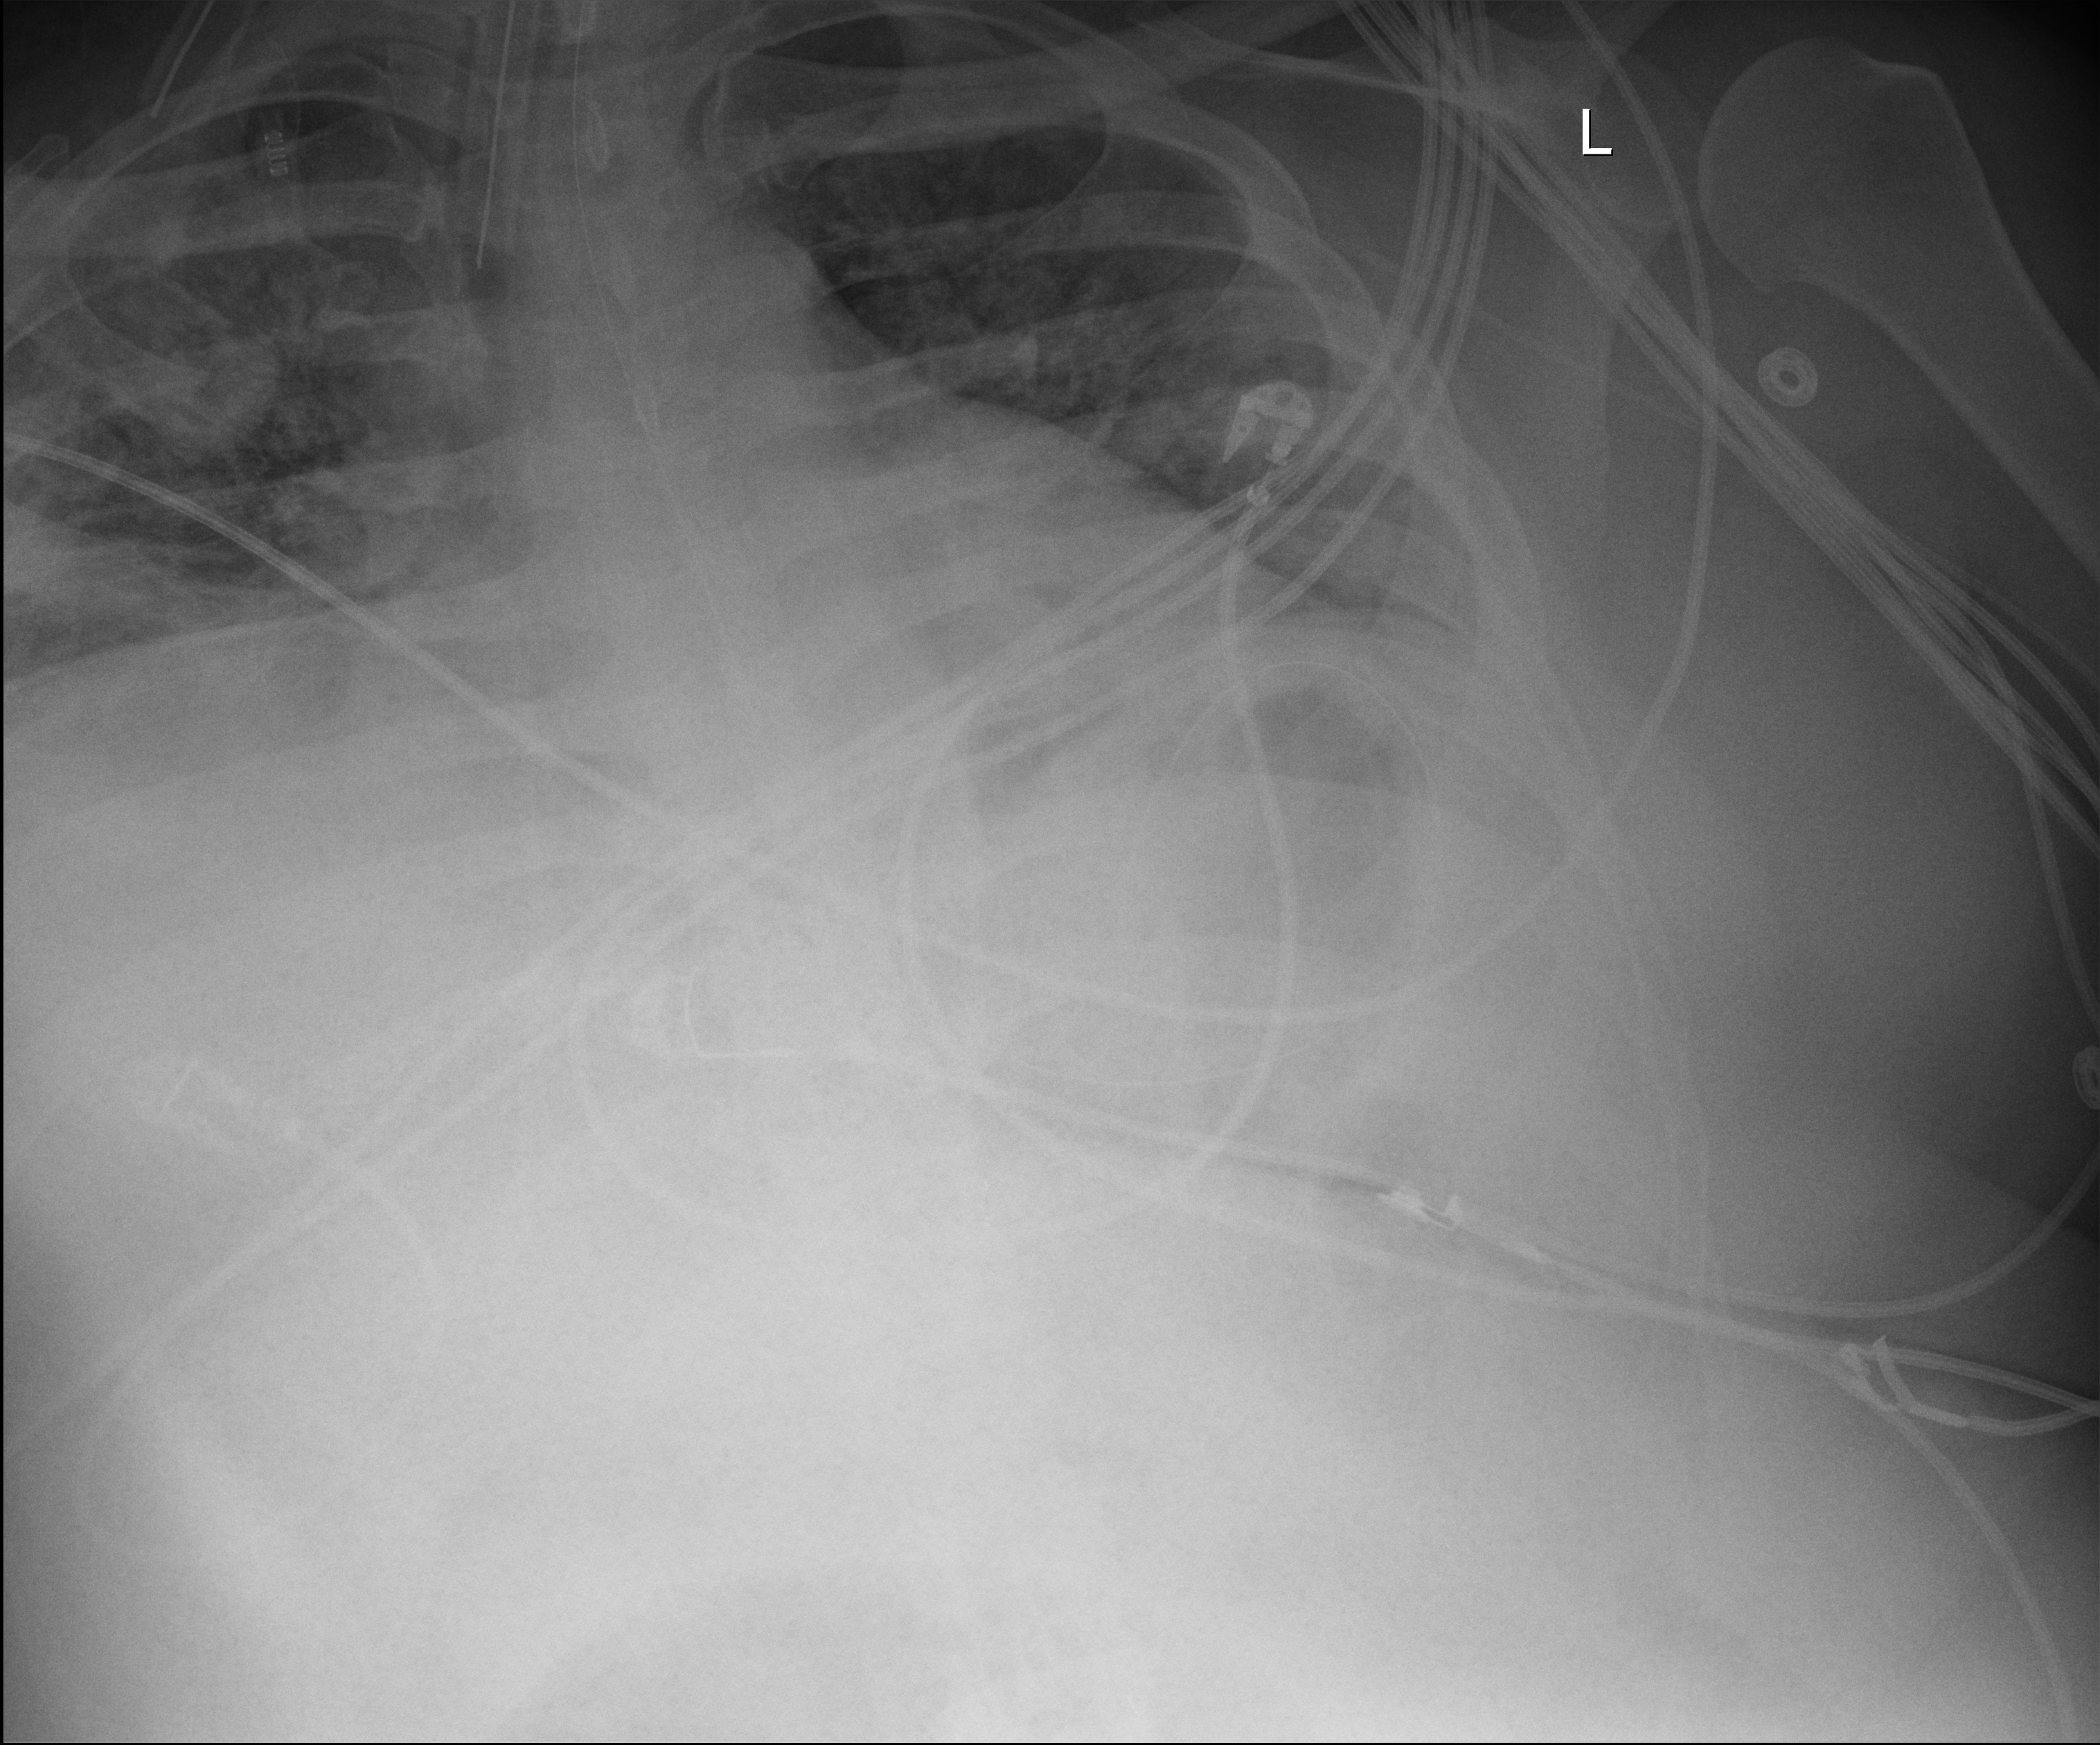
Chest radiograph (digital radiography); anteroposterior (AP) projection. Male patient hospitalised with COVID-19, age 18–59 years.
From the hospital-stay record, not from the radiograph (when in the stay this image was taken is not recorded): admitted to intensive care during this hospital stay: yes.